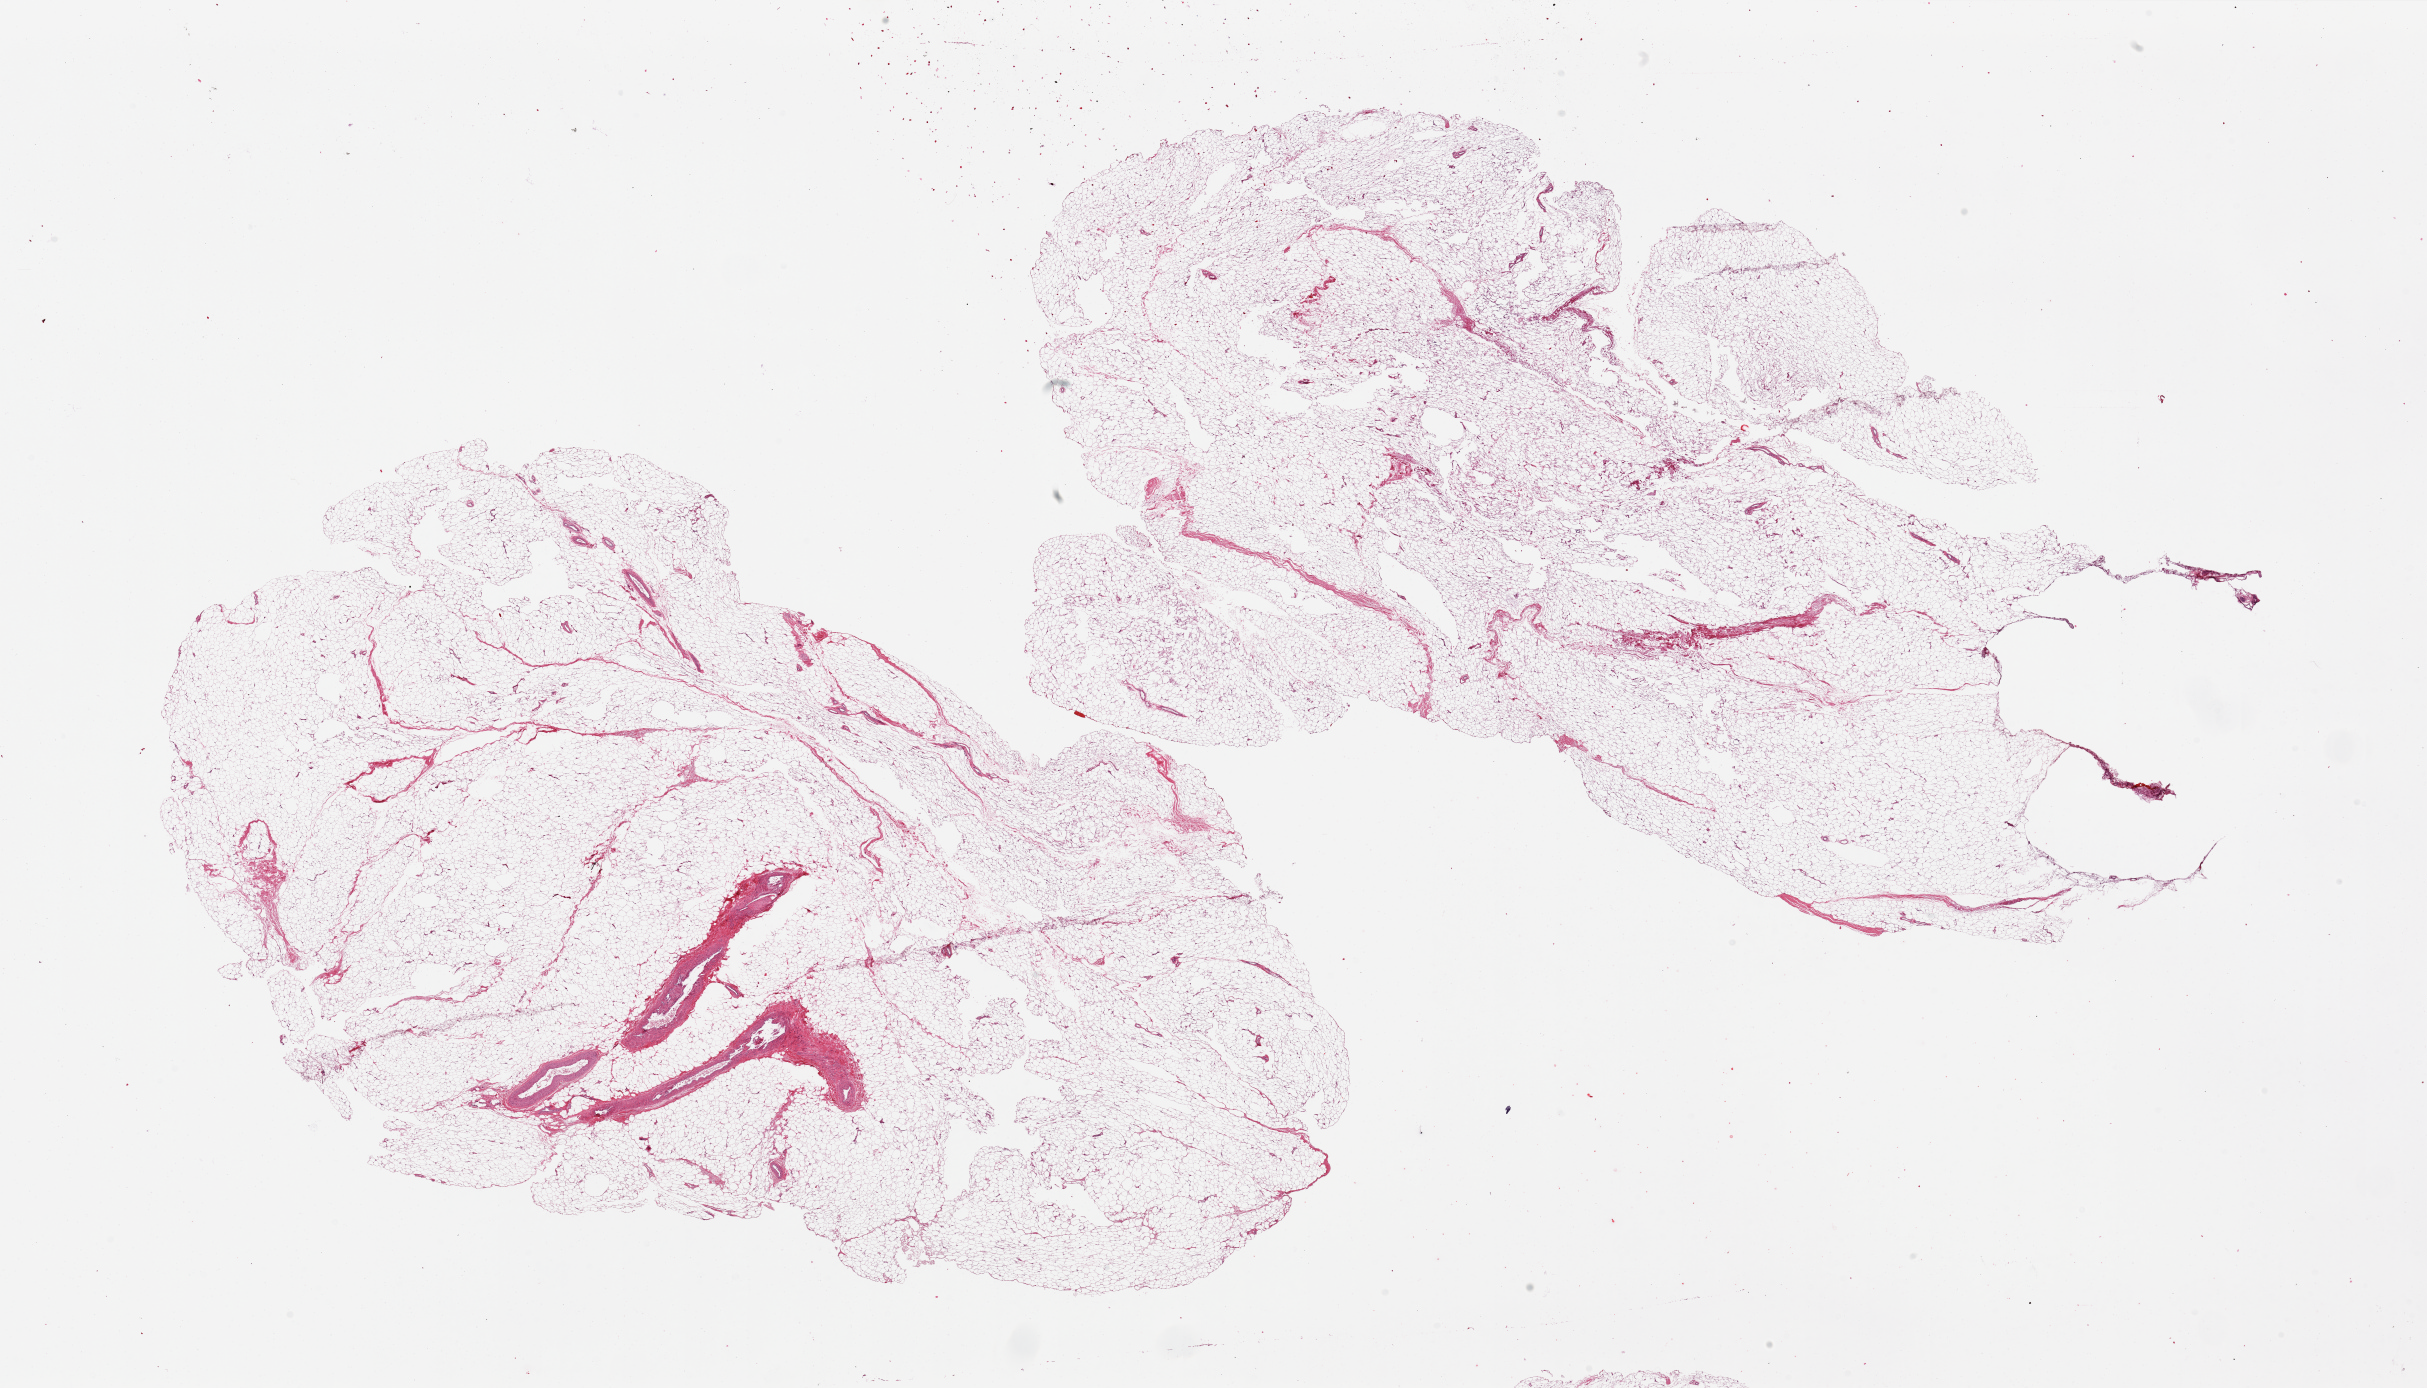
Whole-slide image, H&E stain, shown as a low-resolution overview of the whole scanned area (about 38.4 x 22.0 mm), PAXgene-fixed paraffin-embedded (PFPE) section, sampled site (target tissue): adipose tissue, tissue donor sample.
Reviewer comment on this tissue sample: 2 pieces ~19x12mm ; predominantly intact with minimal fibrous tissue; large vessels present in aliquots.